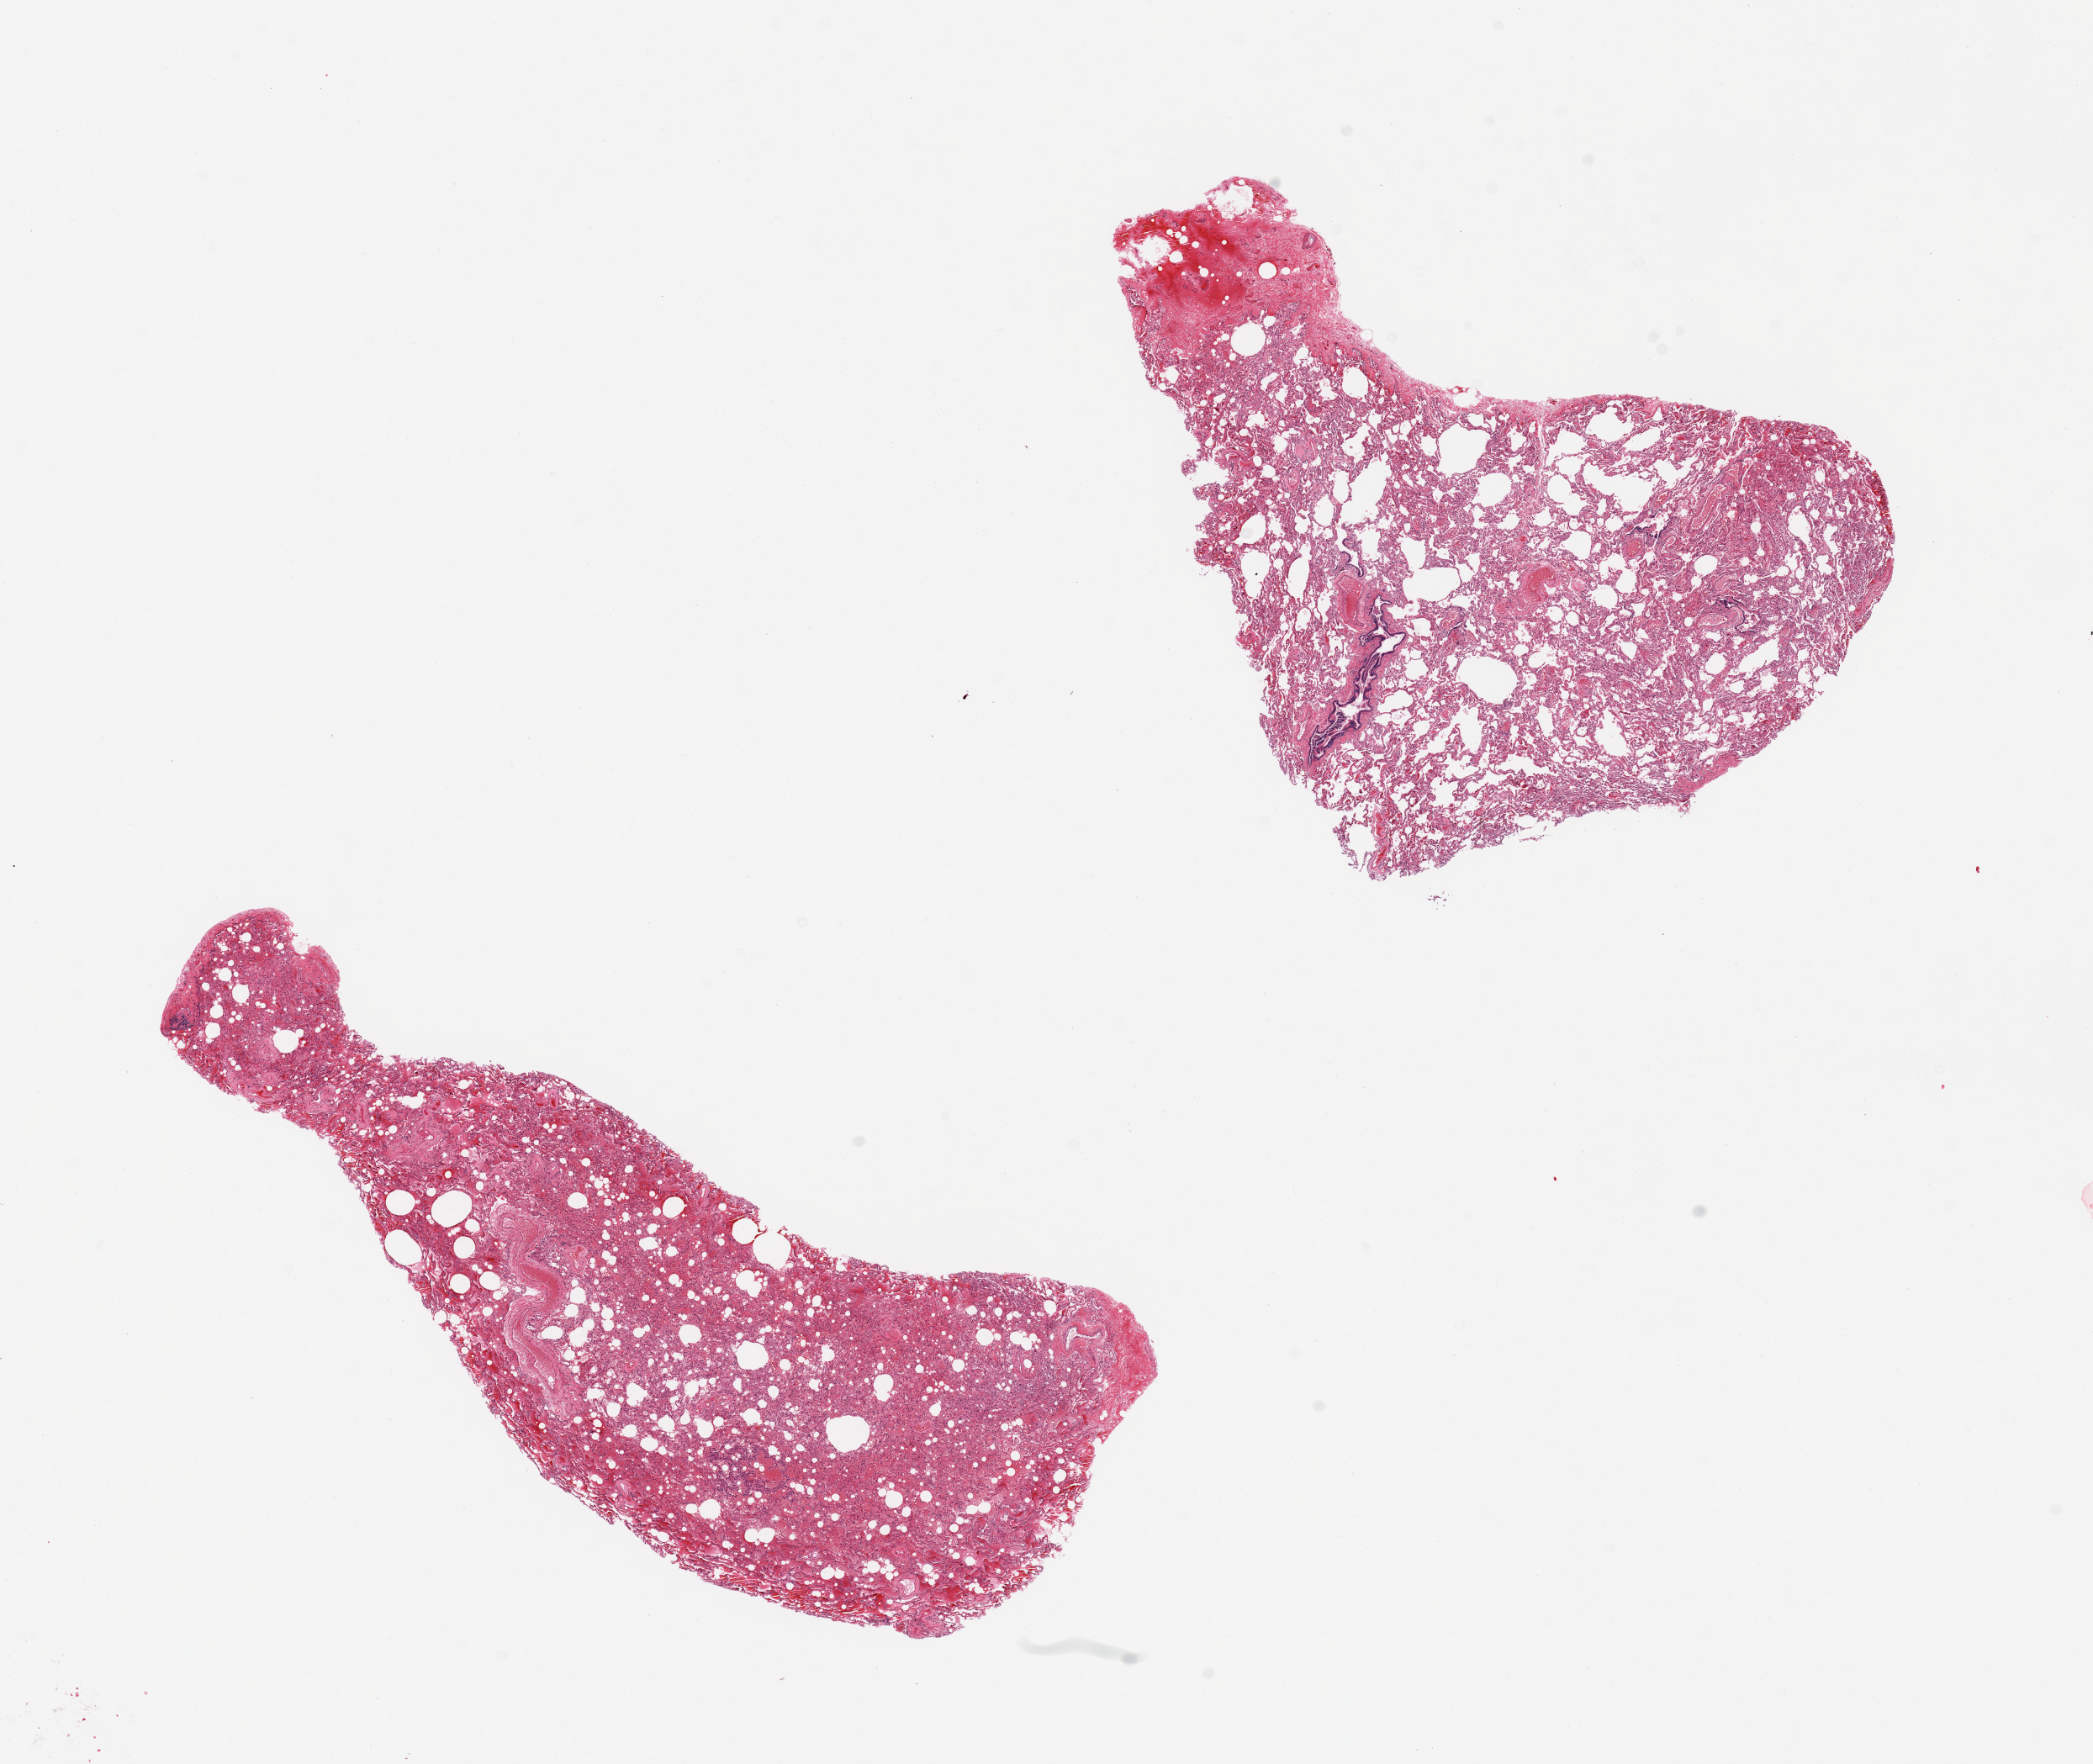
Whole-slide image, haematoxylin and eosin stain, low-resolution overview of the scanned area, about 19.7 x 16.6 mm, PAXgene-fixed, paraffin-embedded tissue, sampled site (target tissue): lung, tissue donor sample.
Reviewer comment on this tissue sample: 2 pieces, hemorrhage and edema.